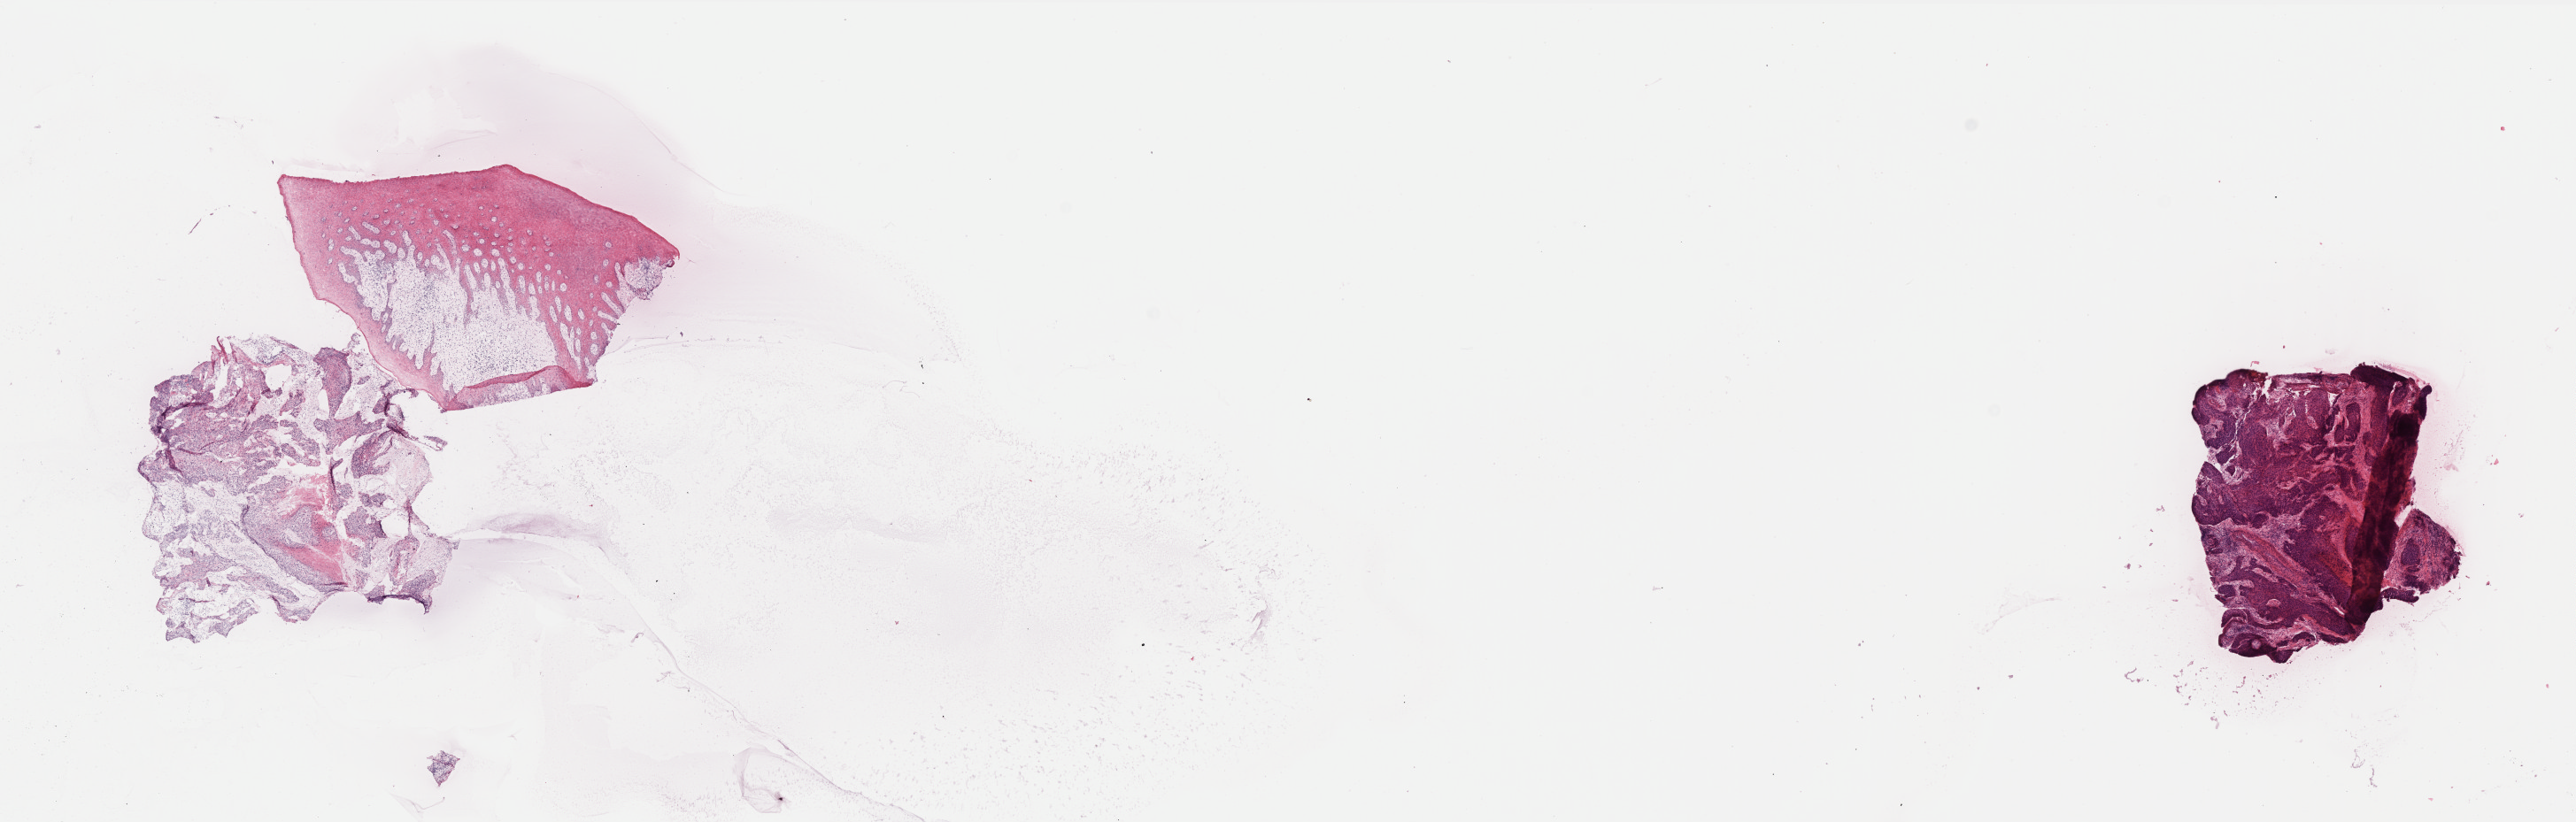
Hematoxylin and eosin (H&E) stained whole-slide image — shown as a low-resolution overview of the whole scanned area (about 23.3 x 7.4 mm, slide scanned at 40x); frozen section; cervix, primary tumour sample. Female patient; age at initial diagnosis 44 years. Histologic grade: G1 (well differentiated). Pathologist review of this section (percent, as recorded): tumour cells 60%, tumour nuclei 60%, normal cells 20%, stromal cells 20%, necrosis 0%. Infiltration values recorded for this section: lymphocyte infiltration 40%, monocyte infiltration 20%, neutrophil infiltration 20%.
FIGO stage: IIIB. Lymph nodes positive (case pathology): 8 of 9 examined. Pathologic diagnosis: Squamous cell carcinoma, NOS (cervix uteri).